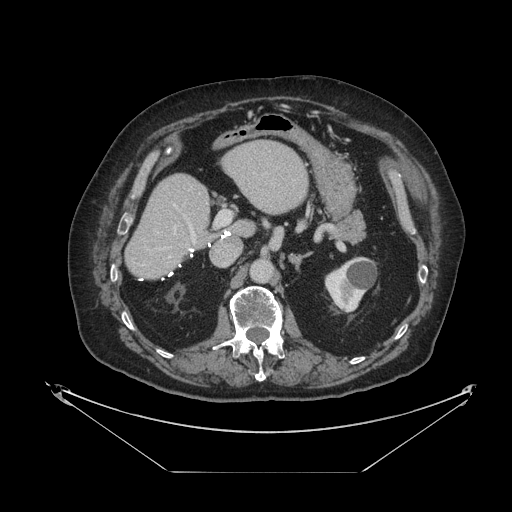
Contrast-enhanced abdominal CT, one axial slice. Position 52 of 121 along the scan axis. Reconstruction kernel STANDARD. 120 kVp. Soft-tissue window (W 400 / L 40 HU). 512 × 512 image matrix, field of view 500 × 500 mm. Male patient, age 68 years. Case-level facts recorded for this patient, not image findings: diagnosis: colorectal cancer liver metastases, imaged before liver resection; multiple liver metastases: no; largest metastasis: 4 cm; disease in both lobes: no.
Outlined on this slice (manually delineated by an expert):
- hepatic veins: bounding box [x1, y1, x2, y2] px = [169, 227, 176, 258]
- liver: [127, 142, 308, 278]
- planned liver remnant (the part of the liver to remain after resection): [127, 142, 308, 278]
- portal vein (with intrahepatic branches): [163, 205, 231, 249]